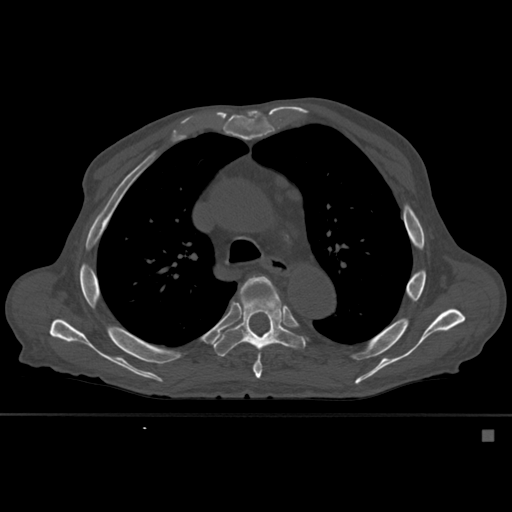
CT including the spine, one axial slice. Slice 390 of 527 in the series (ordered by position). Bone window (W 1800 / L 400 HU). 1.5 mm slice thickness. 512 × 512 image matrix. Patient: male, 78 years. Case-level facts recorded for this patient, not image findings: primary cancer: prostate.
Annotated regions visible in this slice (semi-automatically segmented with operator editing):
- T5 vertebra: bounding box (x1, y1, x2, y2) in pixels: (240, 276, 279, 379)
- T6 vertebra: (214, 276, 304, 357)